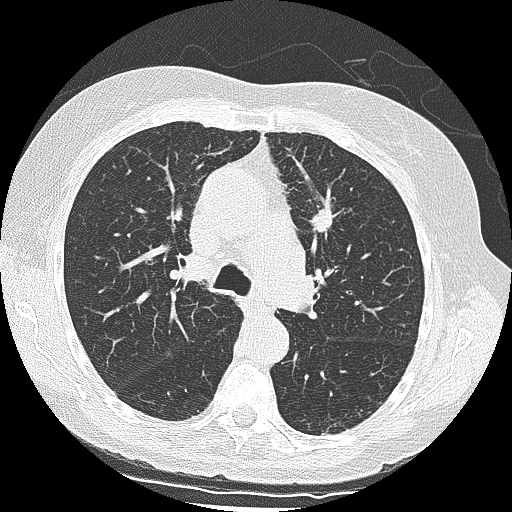
Low-dose screening chest CT, one axial slice. Position 93 of 139 along the scan axis. Reconstruction kernel LUNG. 120 kVp. Lung window (W 1500 / L -600 HU). 2.5 mm slice thickness. 512 × 512 image matrix, field of view 318 × 318 mm.
Structures marked on this image (manually delineated by an expert):
- lesion 1 (tumor, upper lobe of left lung): box from (x=308, y=209) to (x=335, y=235) px